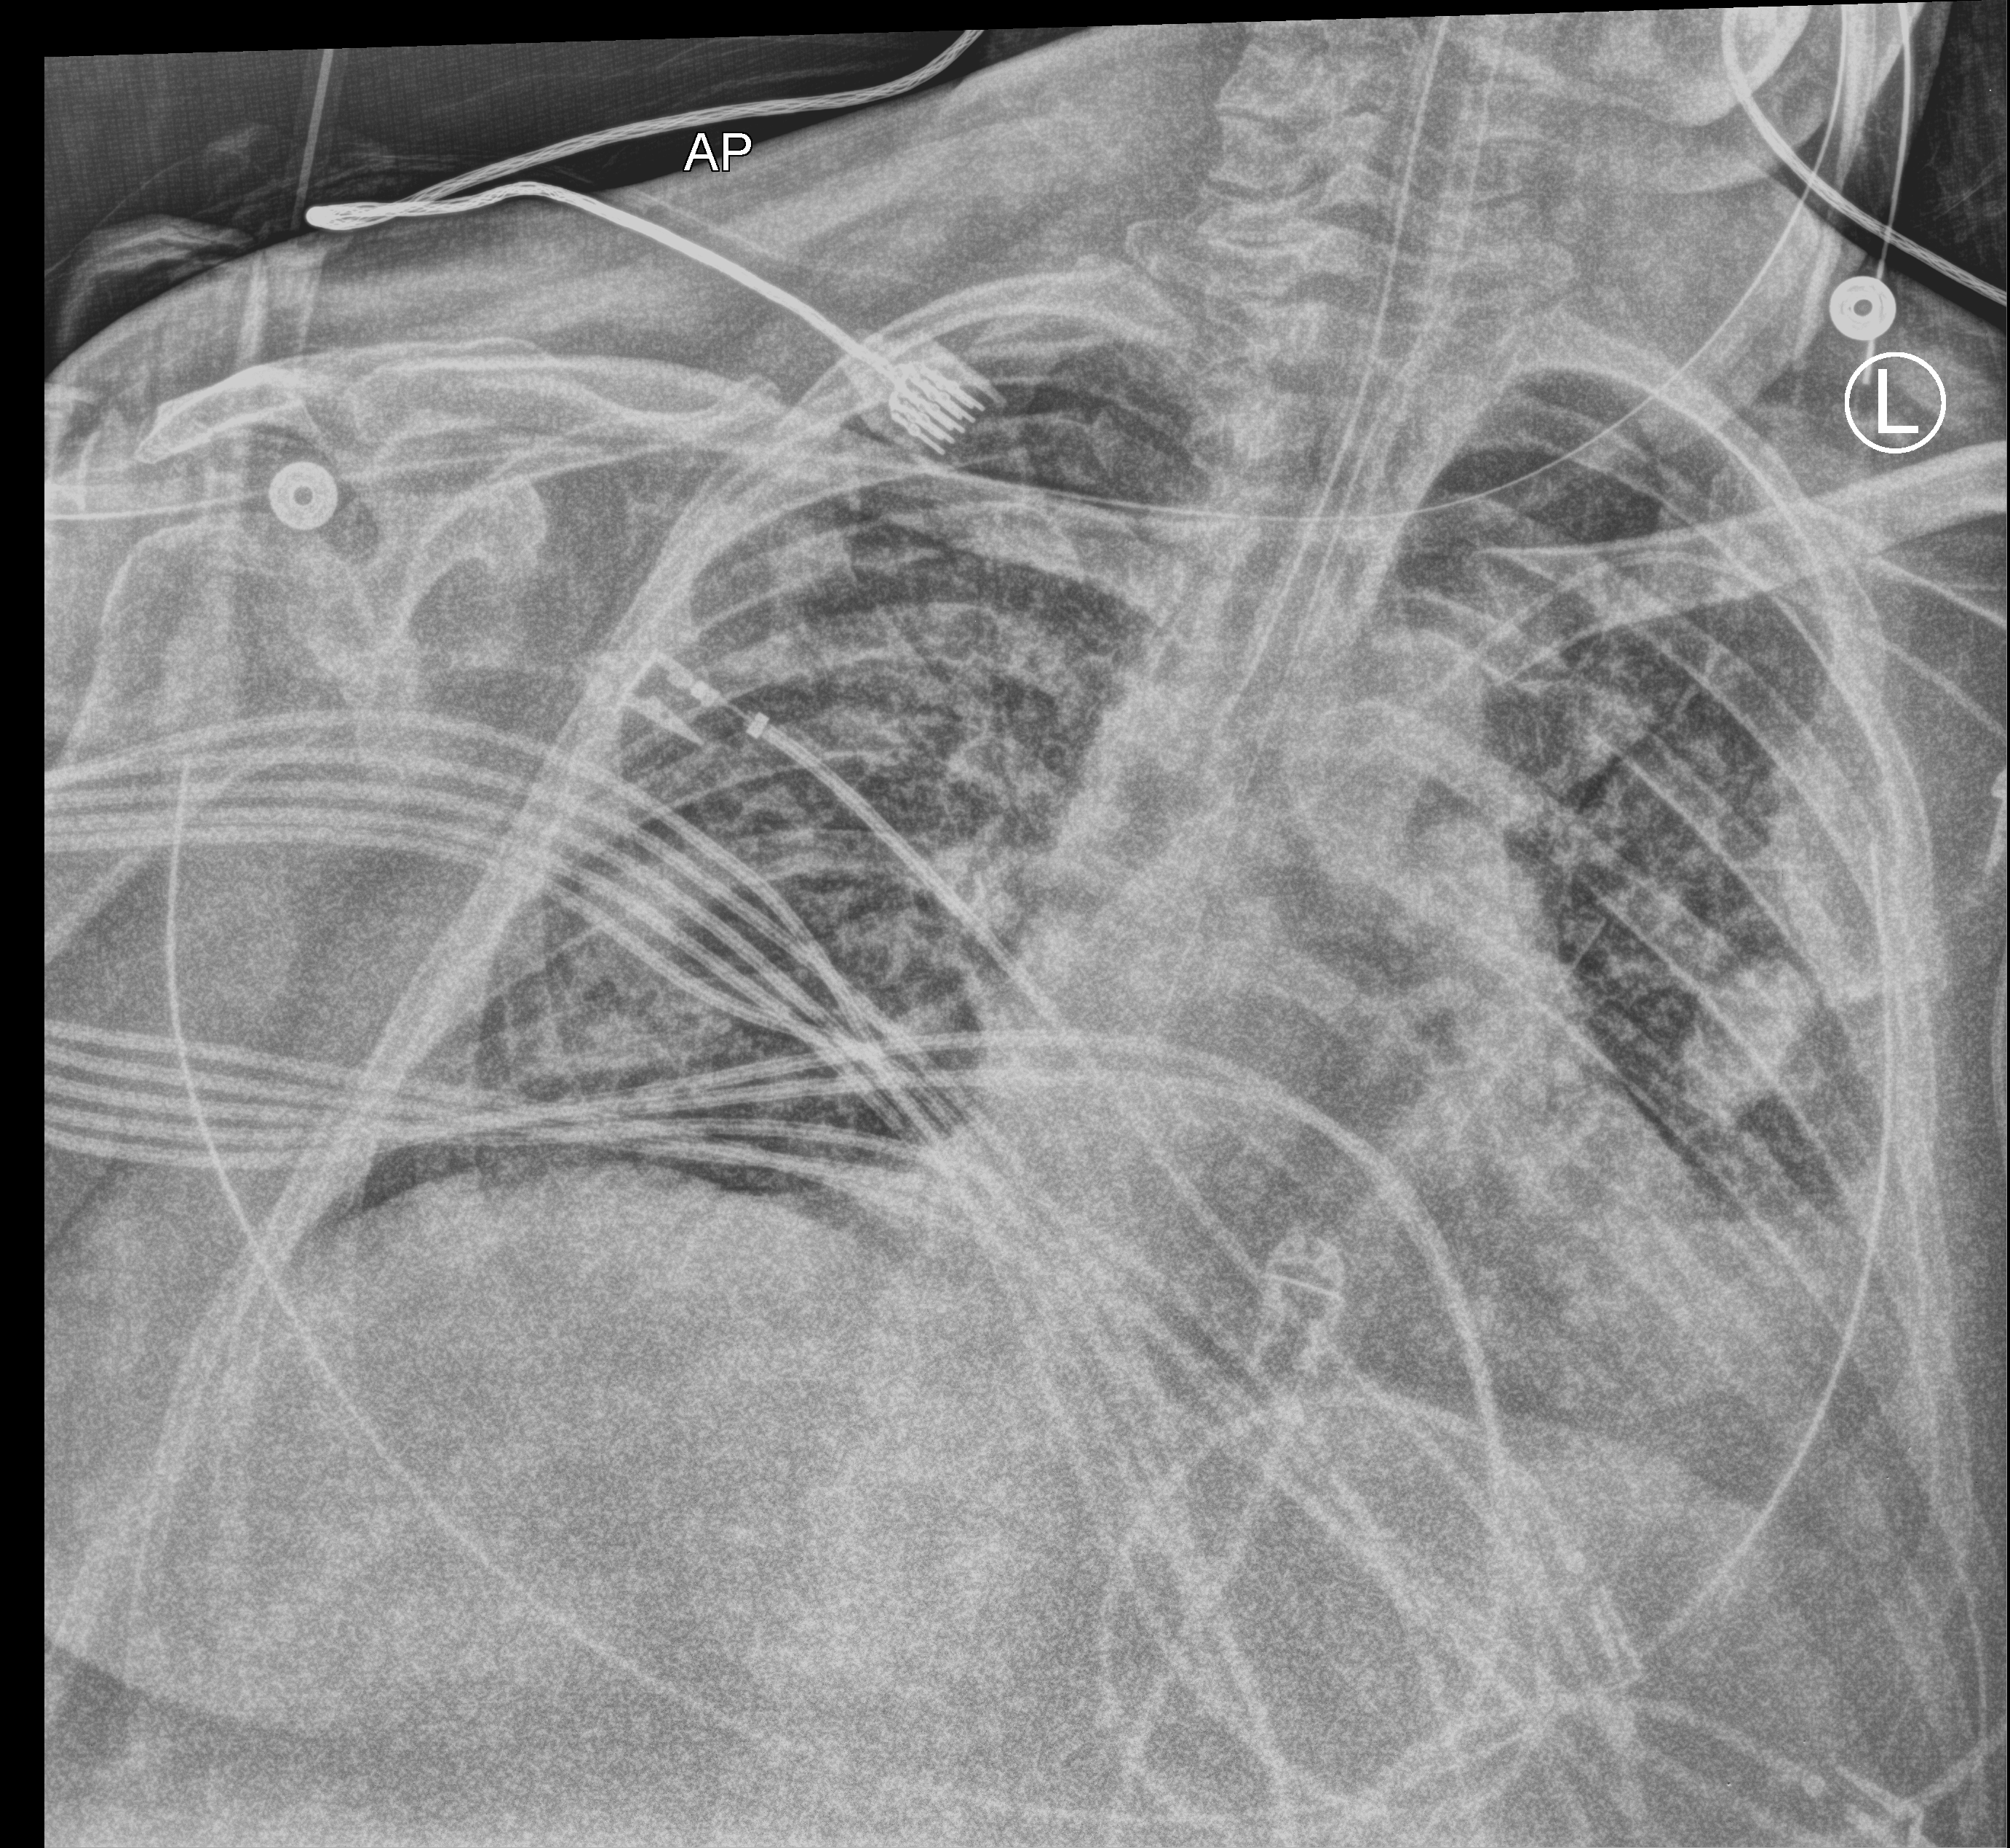
Chest X-ray (portable), anteroposterior (AP) projection. Patient hospitalised with COVID-19; male, aged 18–59 years.
From the hospital-stay record, not from the radiograph (when in the stay this image was taken is not recorded):
- length of hospital stay: 39 days
- admitted to intensive care during this hospital stay: yes